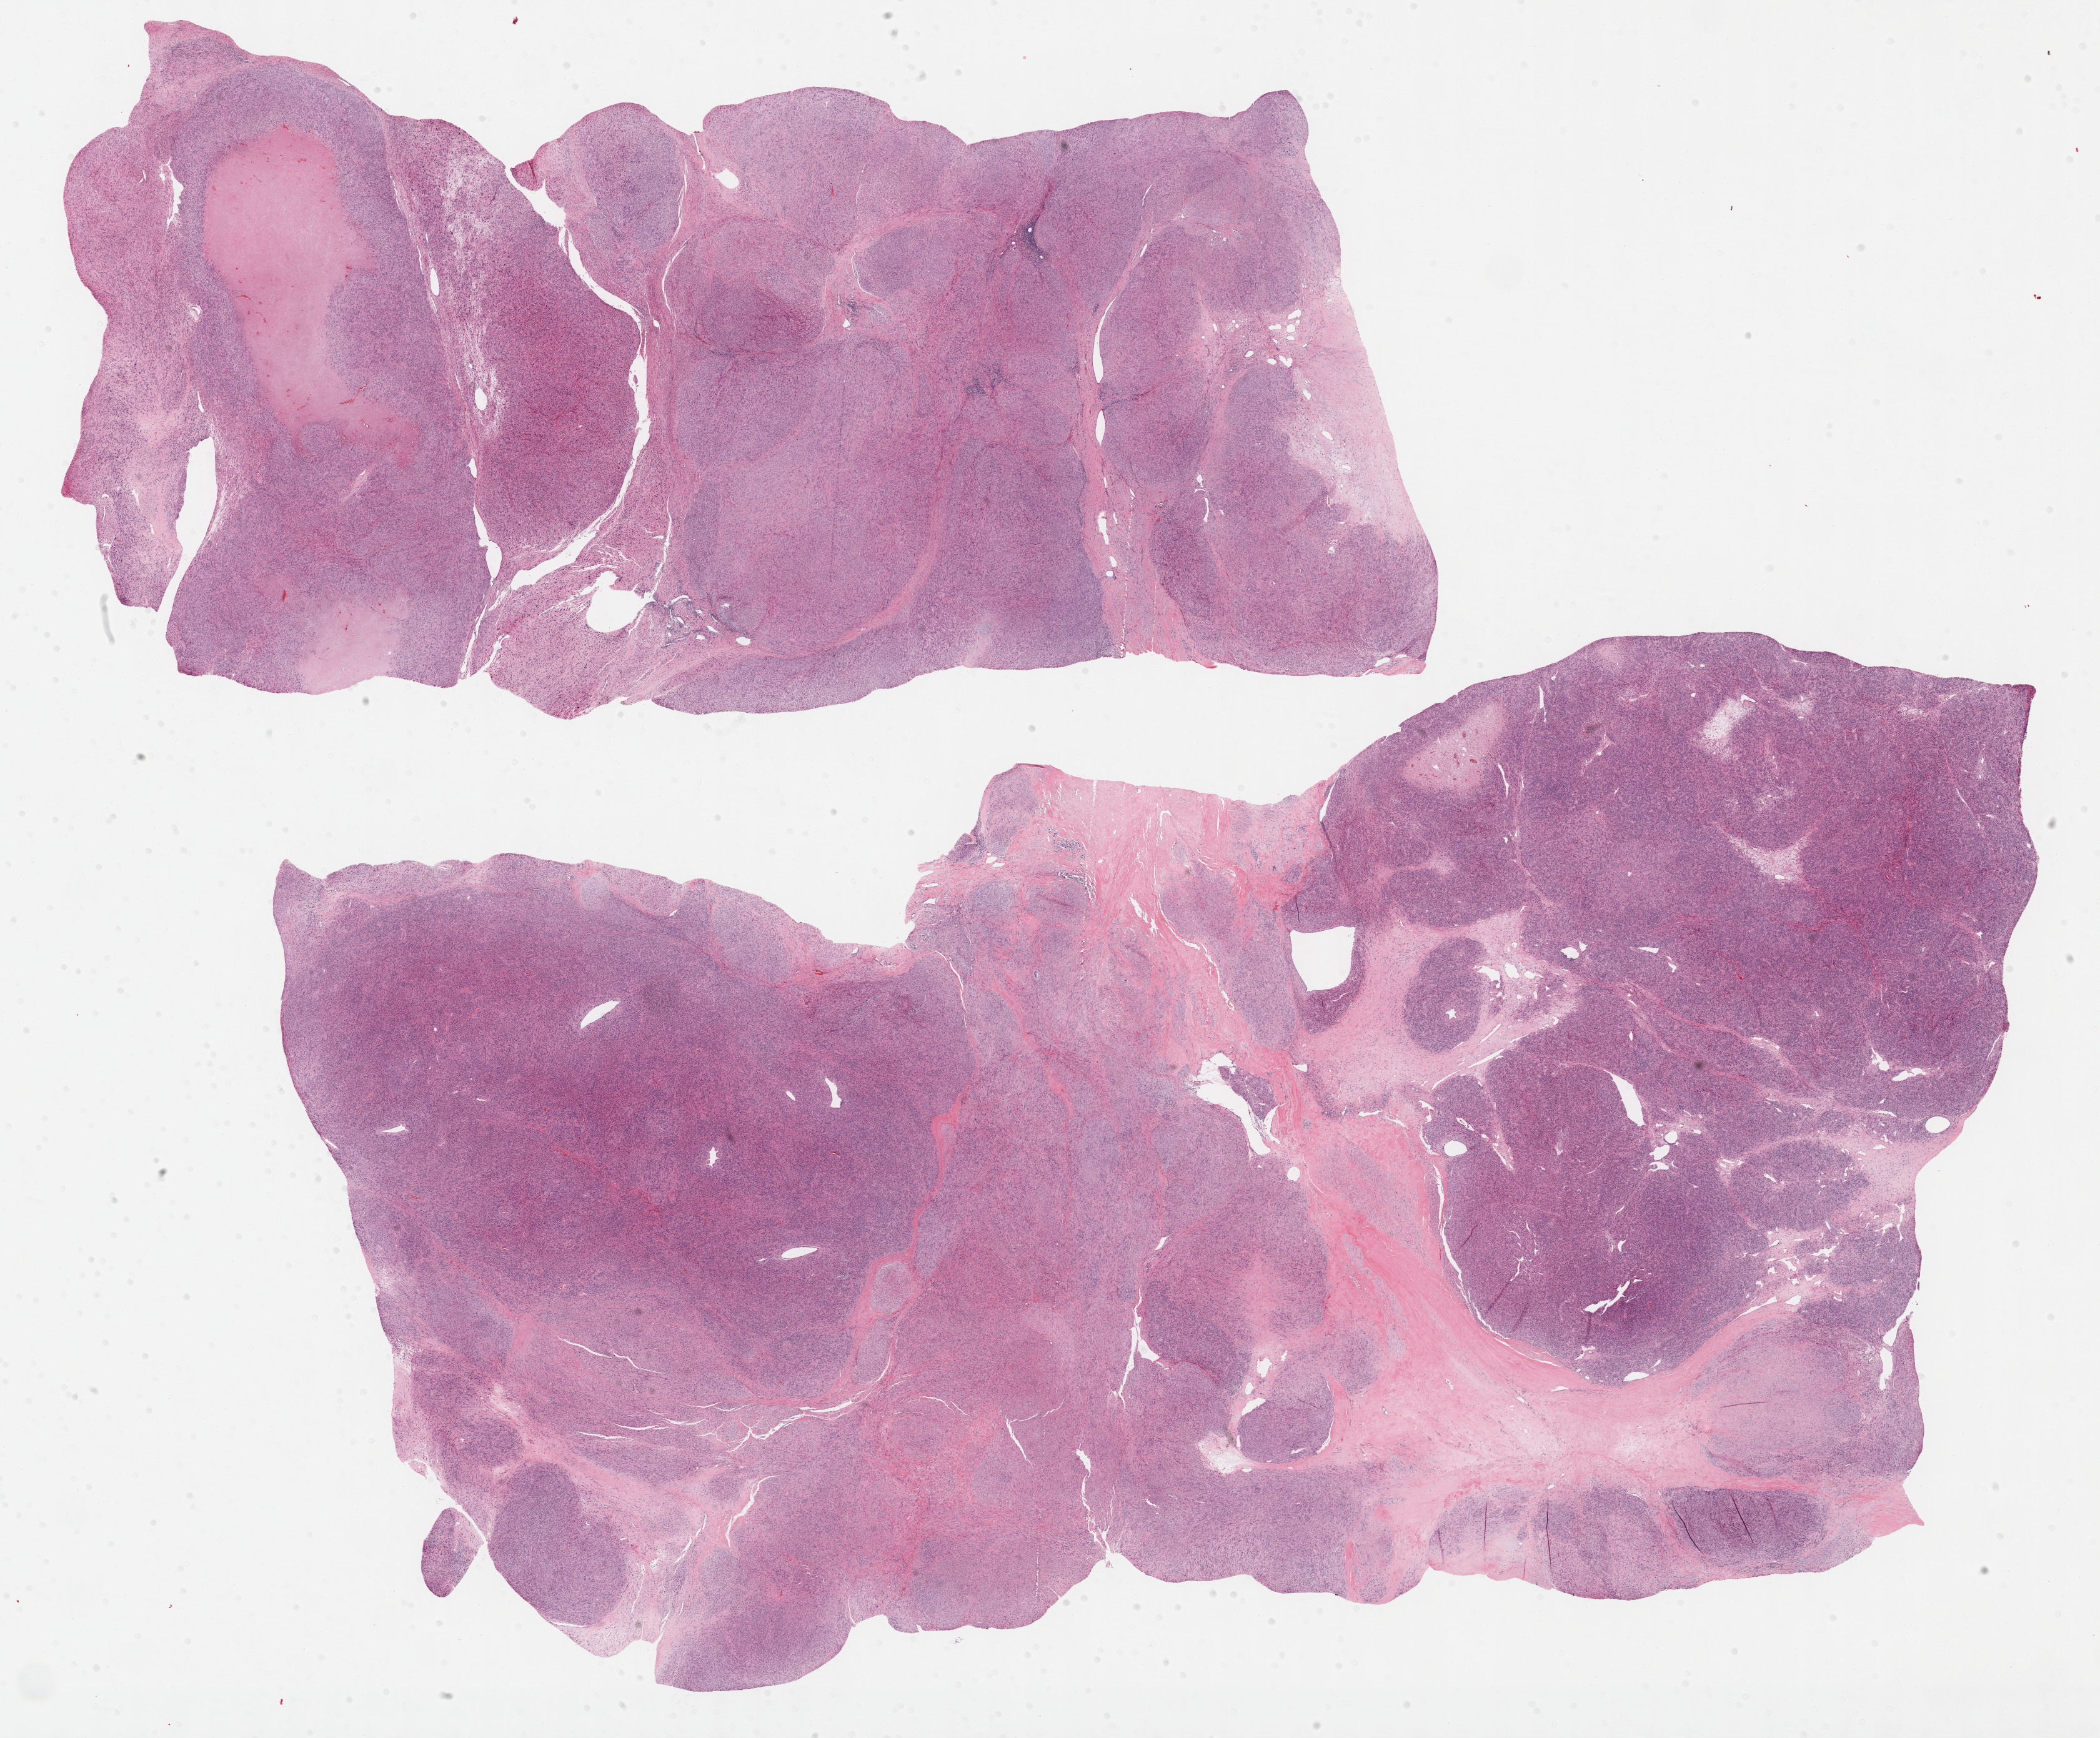
Whole-slide histology image, H&E-stained — whole scanned area (about 27.2 x 22.5 mm) shown as a low-resolution overview. Formalin-fixed paraffin-embedded (FFPE) diagnostic section. Sample: primary tumour, retroperitoneum and peritoneum. Patient: female, age at initial diagnosis 56 years.
Diagnosis: Leiomyosarcoma, NOS.